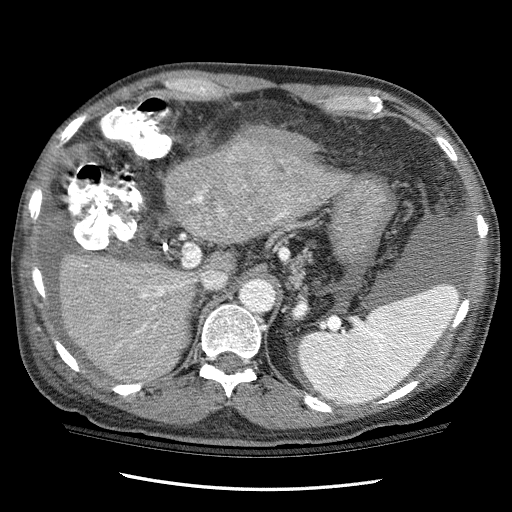
Contrast-enhanced abdominal CT (liver protocol), one axial slice; slice 70 of 114 in the series (ordered by position); reconstruction kernel STANDARD; one of 3 acquisitions stored at this slice position; soft-tissue window (W 400 / L 40 HU); 2.5 mm slice thickness; 512 × 512 image matrix, field of view 360 × 360 mm. Case-level facts recorded for this patient, not image findings: diagnosis: hepatocellular carcinoma (patient treated with transarterial chemoembolisation; whether this scan precedes or follows treatment is not stated here); TNM stage (as recorded): Stage-I; Child-Pugh class: C.
Structures marked on this image (semi-automatic segmentation, software-assisted and operator-edited):
- liver parenchyma outside the tumour (the mass and vessels are separate outlines, so this box may not span the whole liver): bounding box [x1, y1, x2, y2] px = [60, 145, 351, 382]
- mass: [227, 125, 325, 194]
- liver vessels: [84, 191, 289, 333]